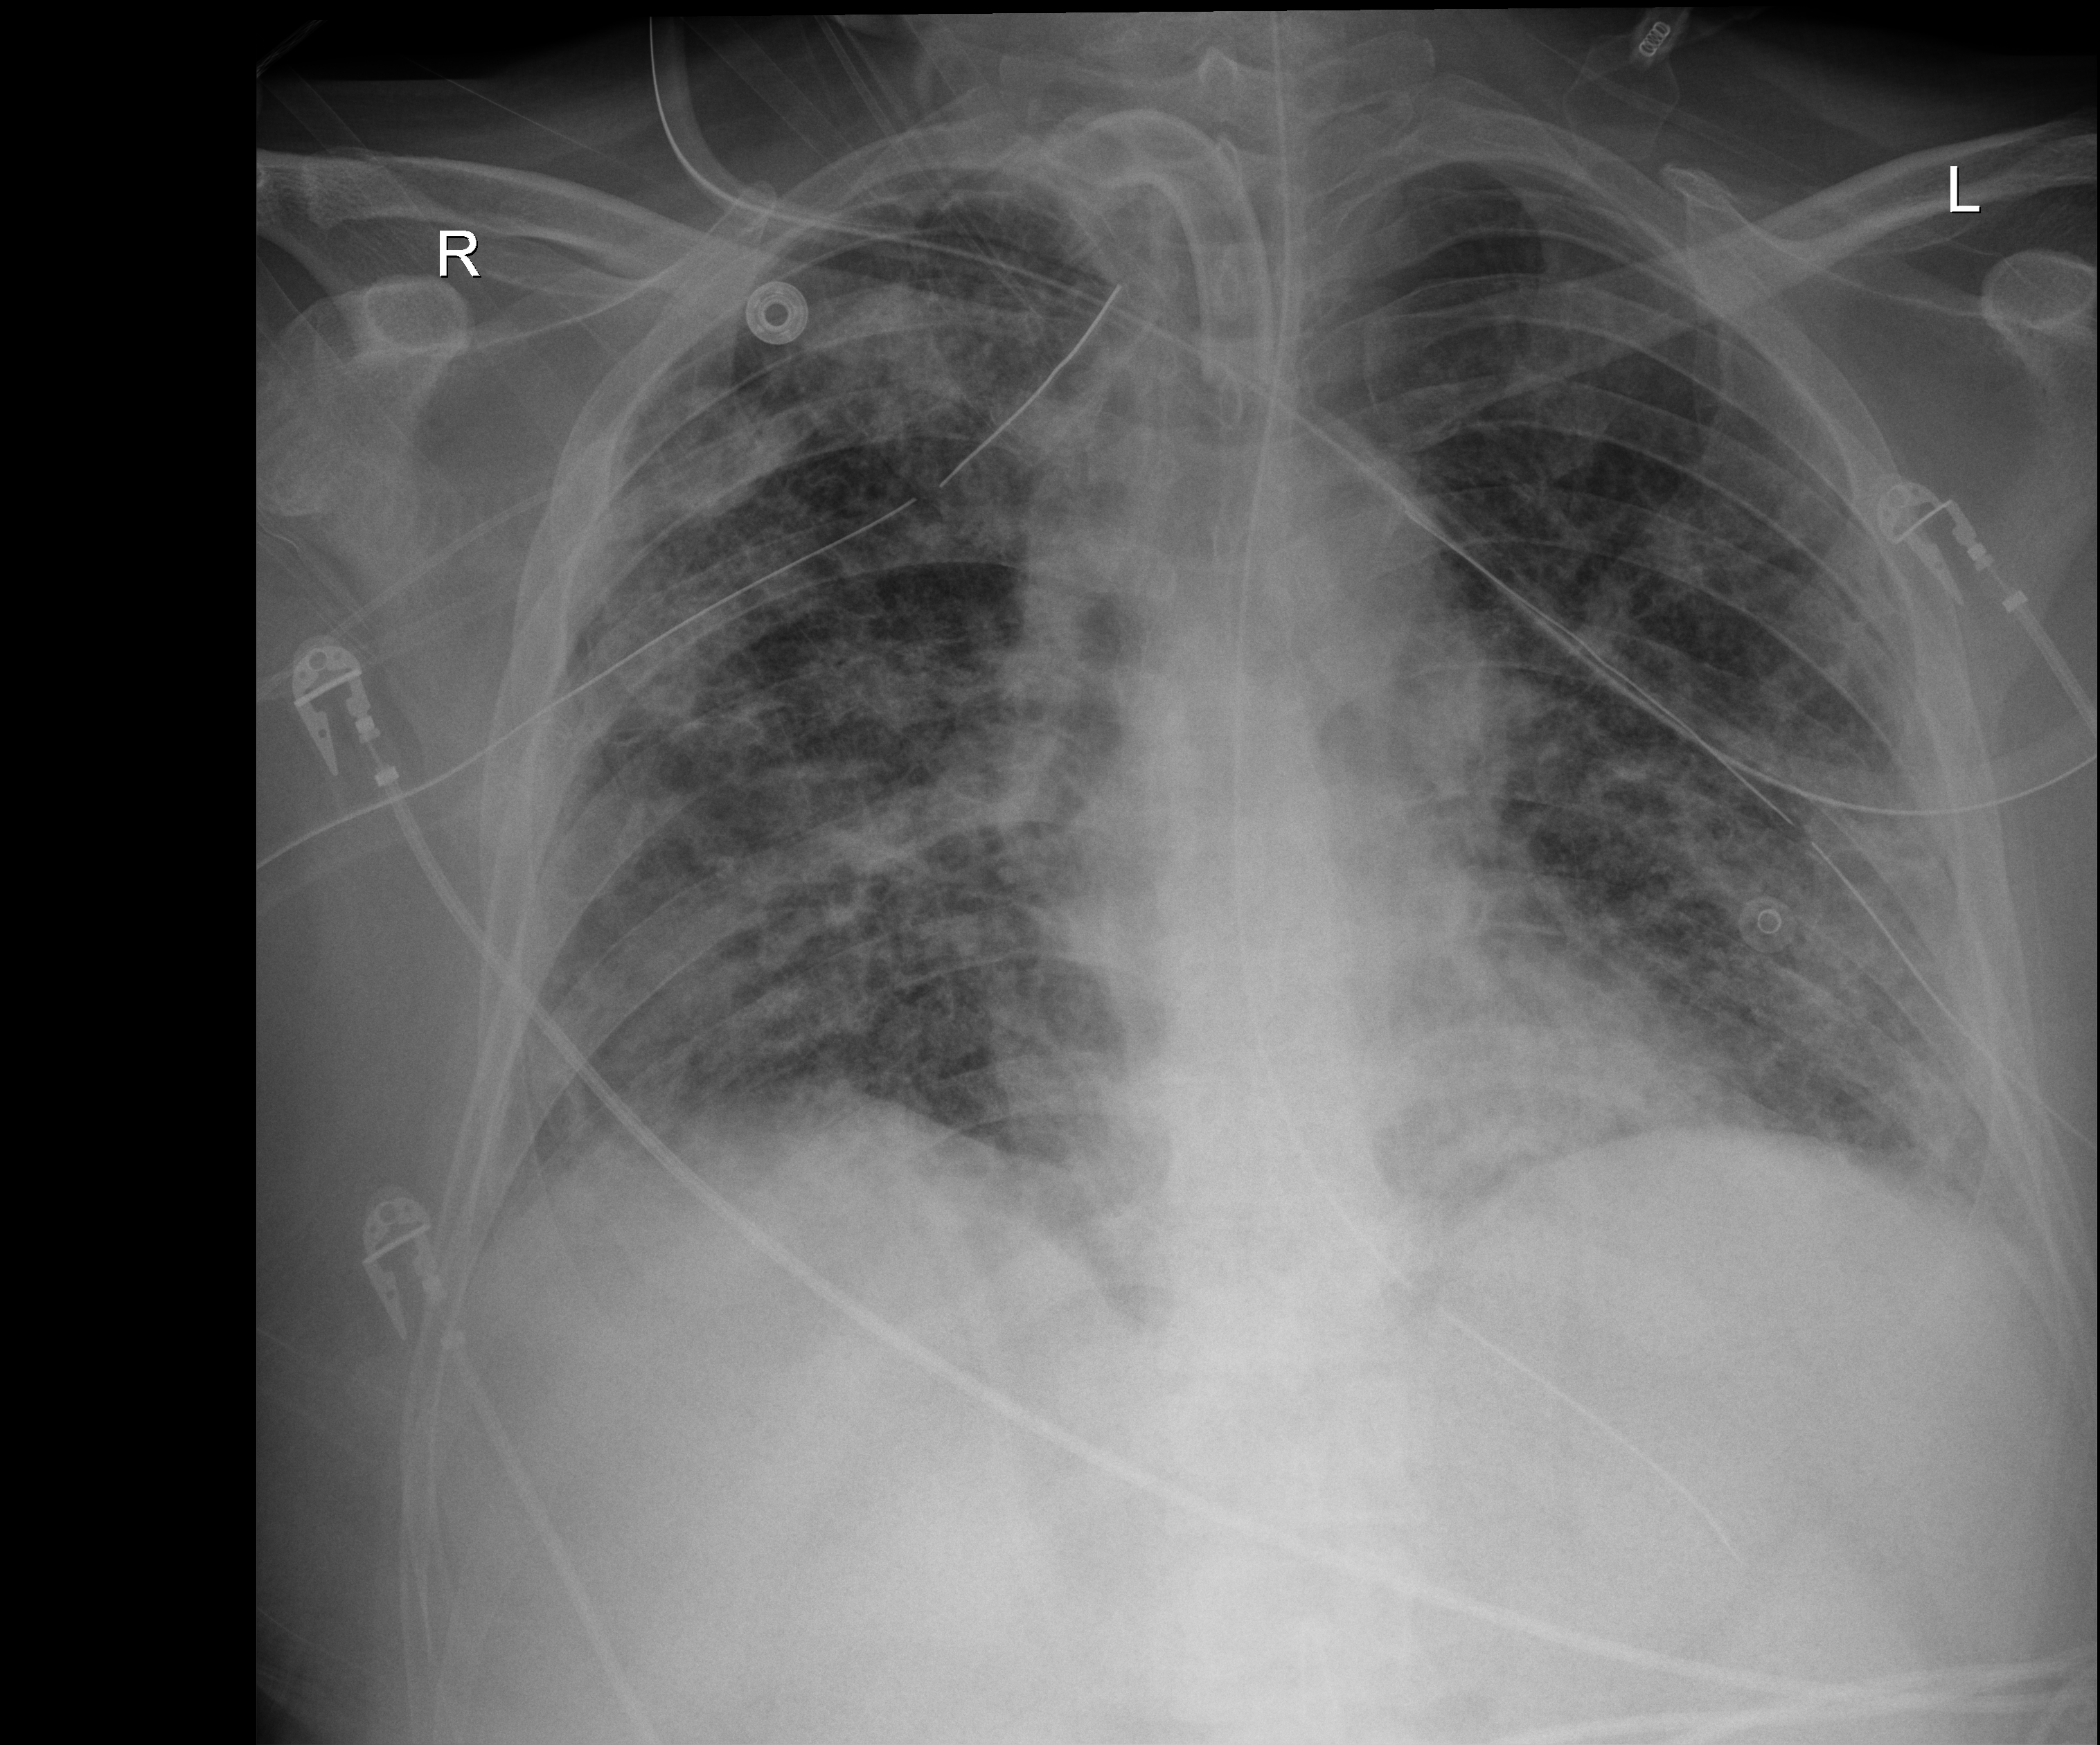
Chest X-ray (portable), anteroposterior (AP) projection. Male patient hospitalised with COVID-19, age 18–59 years.
Admission-level facts for this patient (not findings on this image; timing relative to this image not recorded):
- length of hospital stay: 63 days
- hypertension (admission record): yes